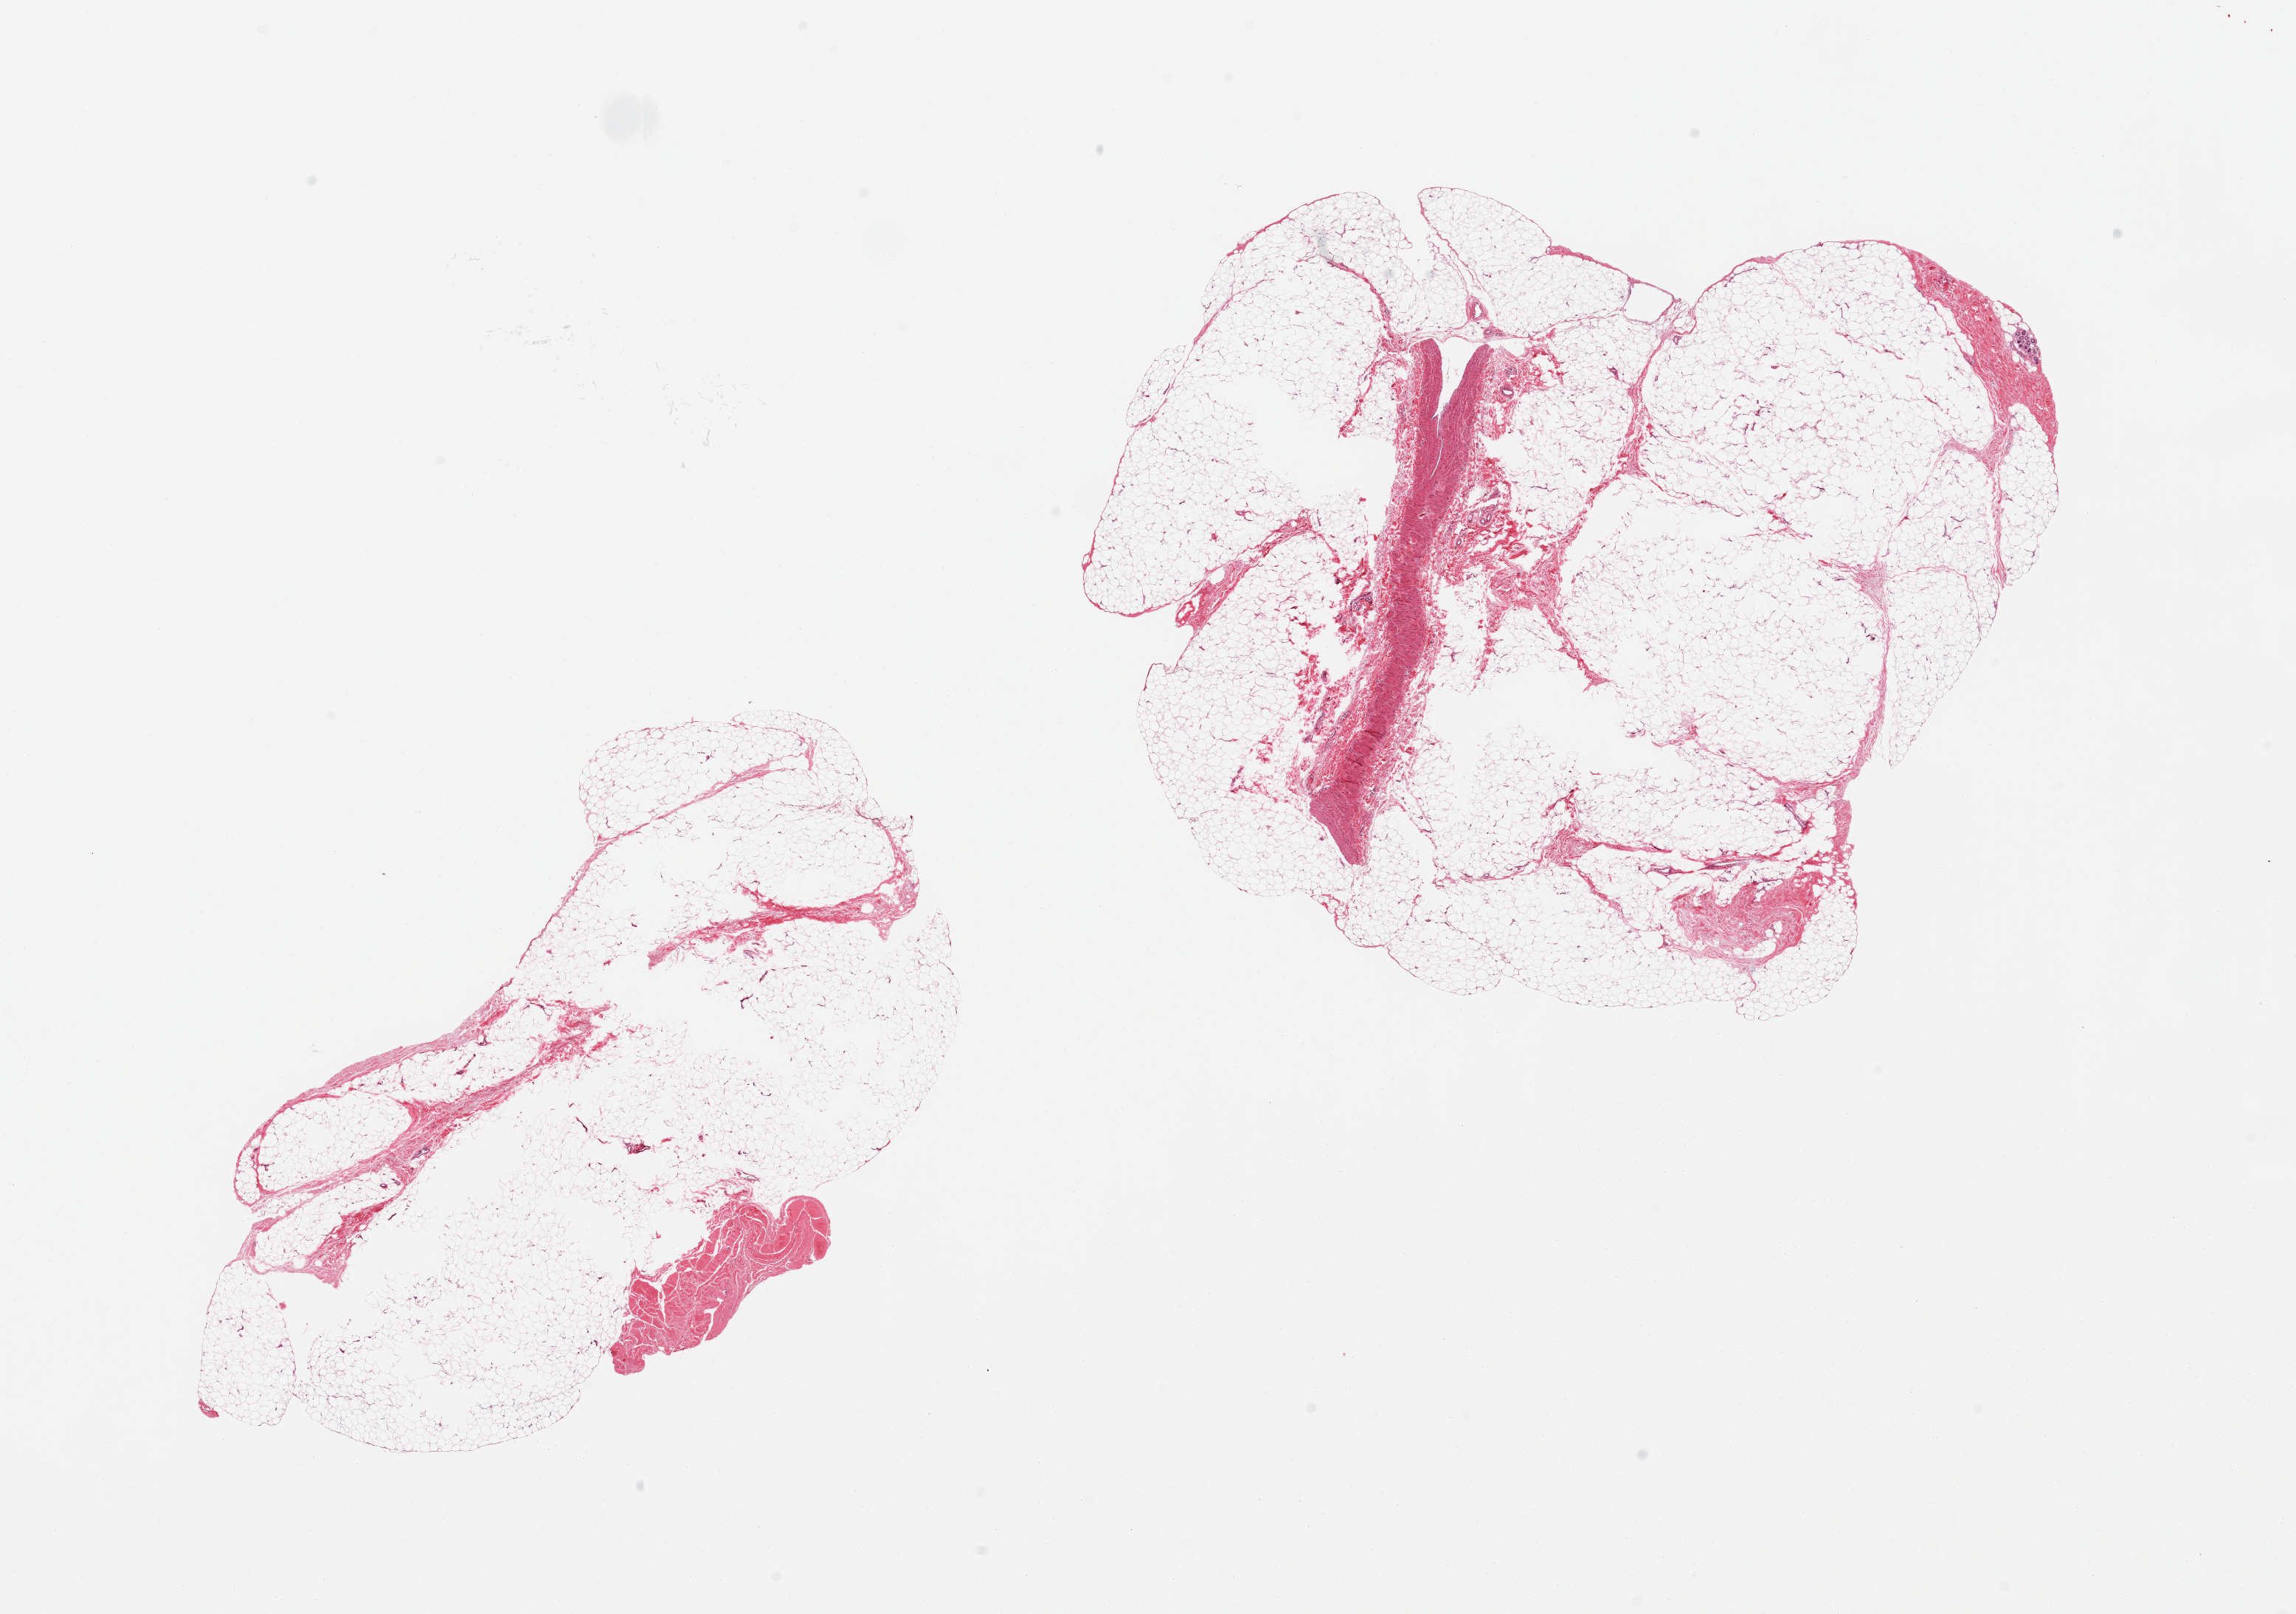
Whole-slide image, H&E stain — low-resolution overview of the scanned area, about 24.6 x 17.3 mm (from a 20x scan), PAXgene-fixed, paraffin-embedded tissue, sampled site (target tissue): adipose tissue, donor tissue sample. Male donor.
Review note (as recorded): 2 pieces, adipose and fibrovascular tissue with small focus of sweat glands.